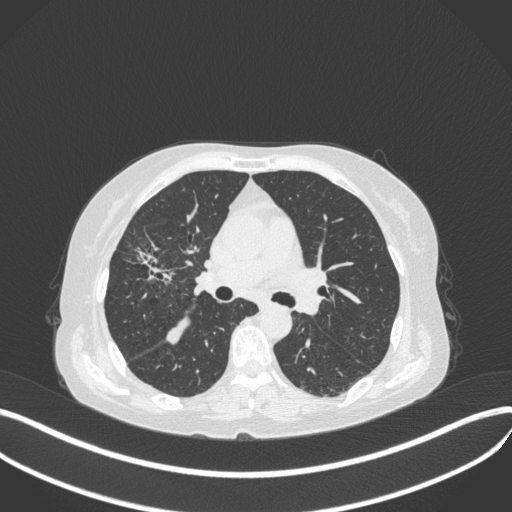
Chest CT, one axial slice; position 235 of 429 along the scan axis; 120 kVp; lung window (W 1500 / L -600 HU); 1 mm slice thickness; 512 × 512 image matrix, field of view 400 × 400 mm. Patient: female, 69 years. Case-level facts recorded for this patient, not image findings: clinical TNM (as recorded): T1b N3 M0.
Annotated regions visible in this slice (bounding box drawn by a radiologist):
- lung tumour (recorded histology: small cell carcinoma): bounding box (x1, y1, x2, y2) in pixels: (121, 236, 179, 287)